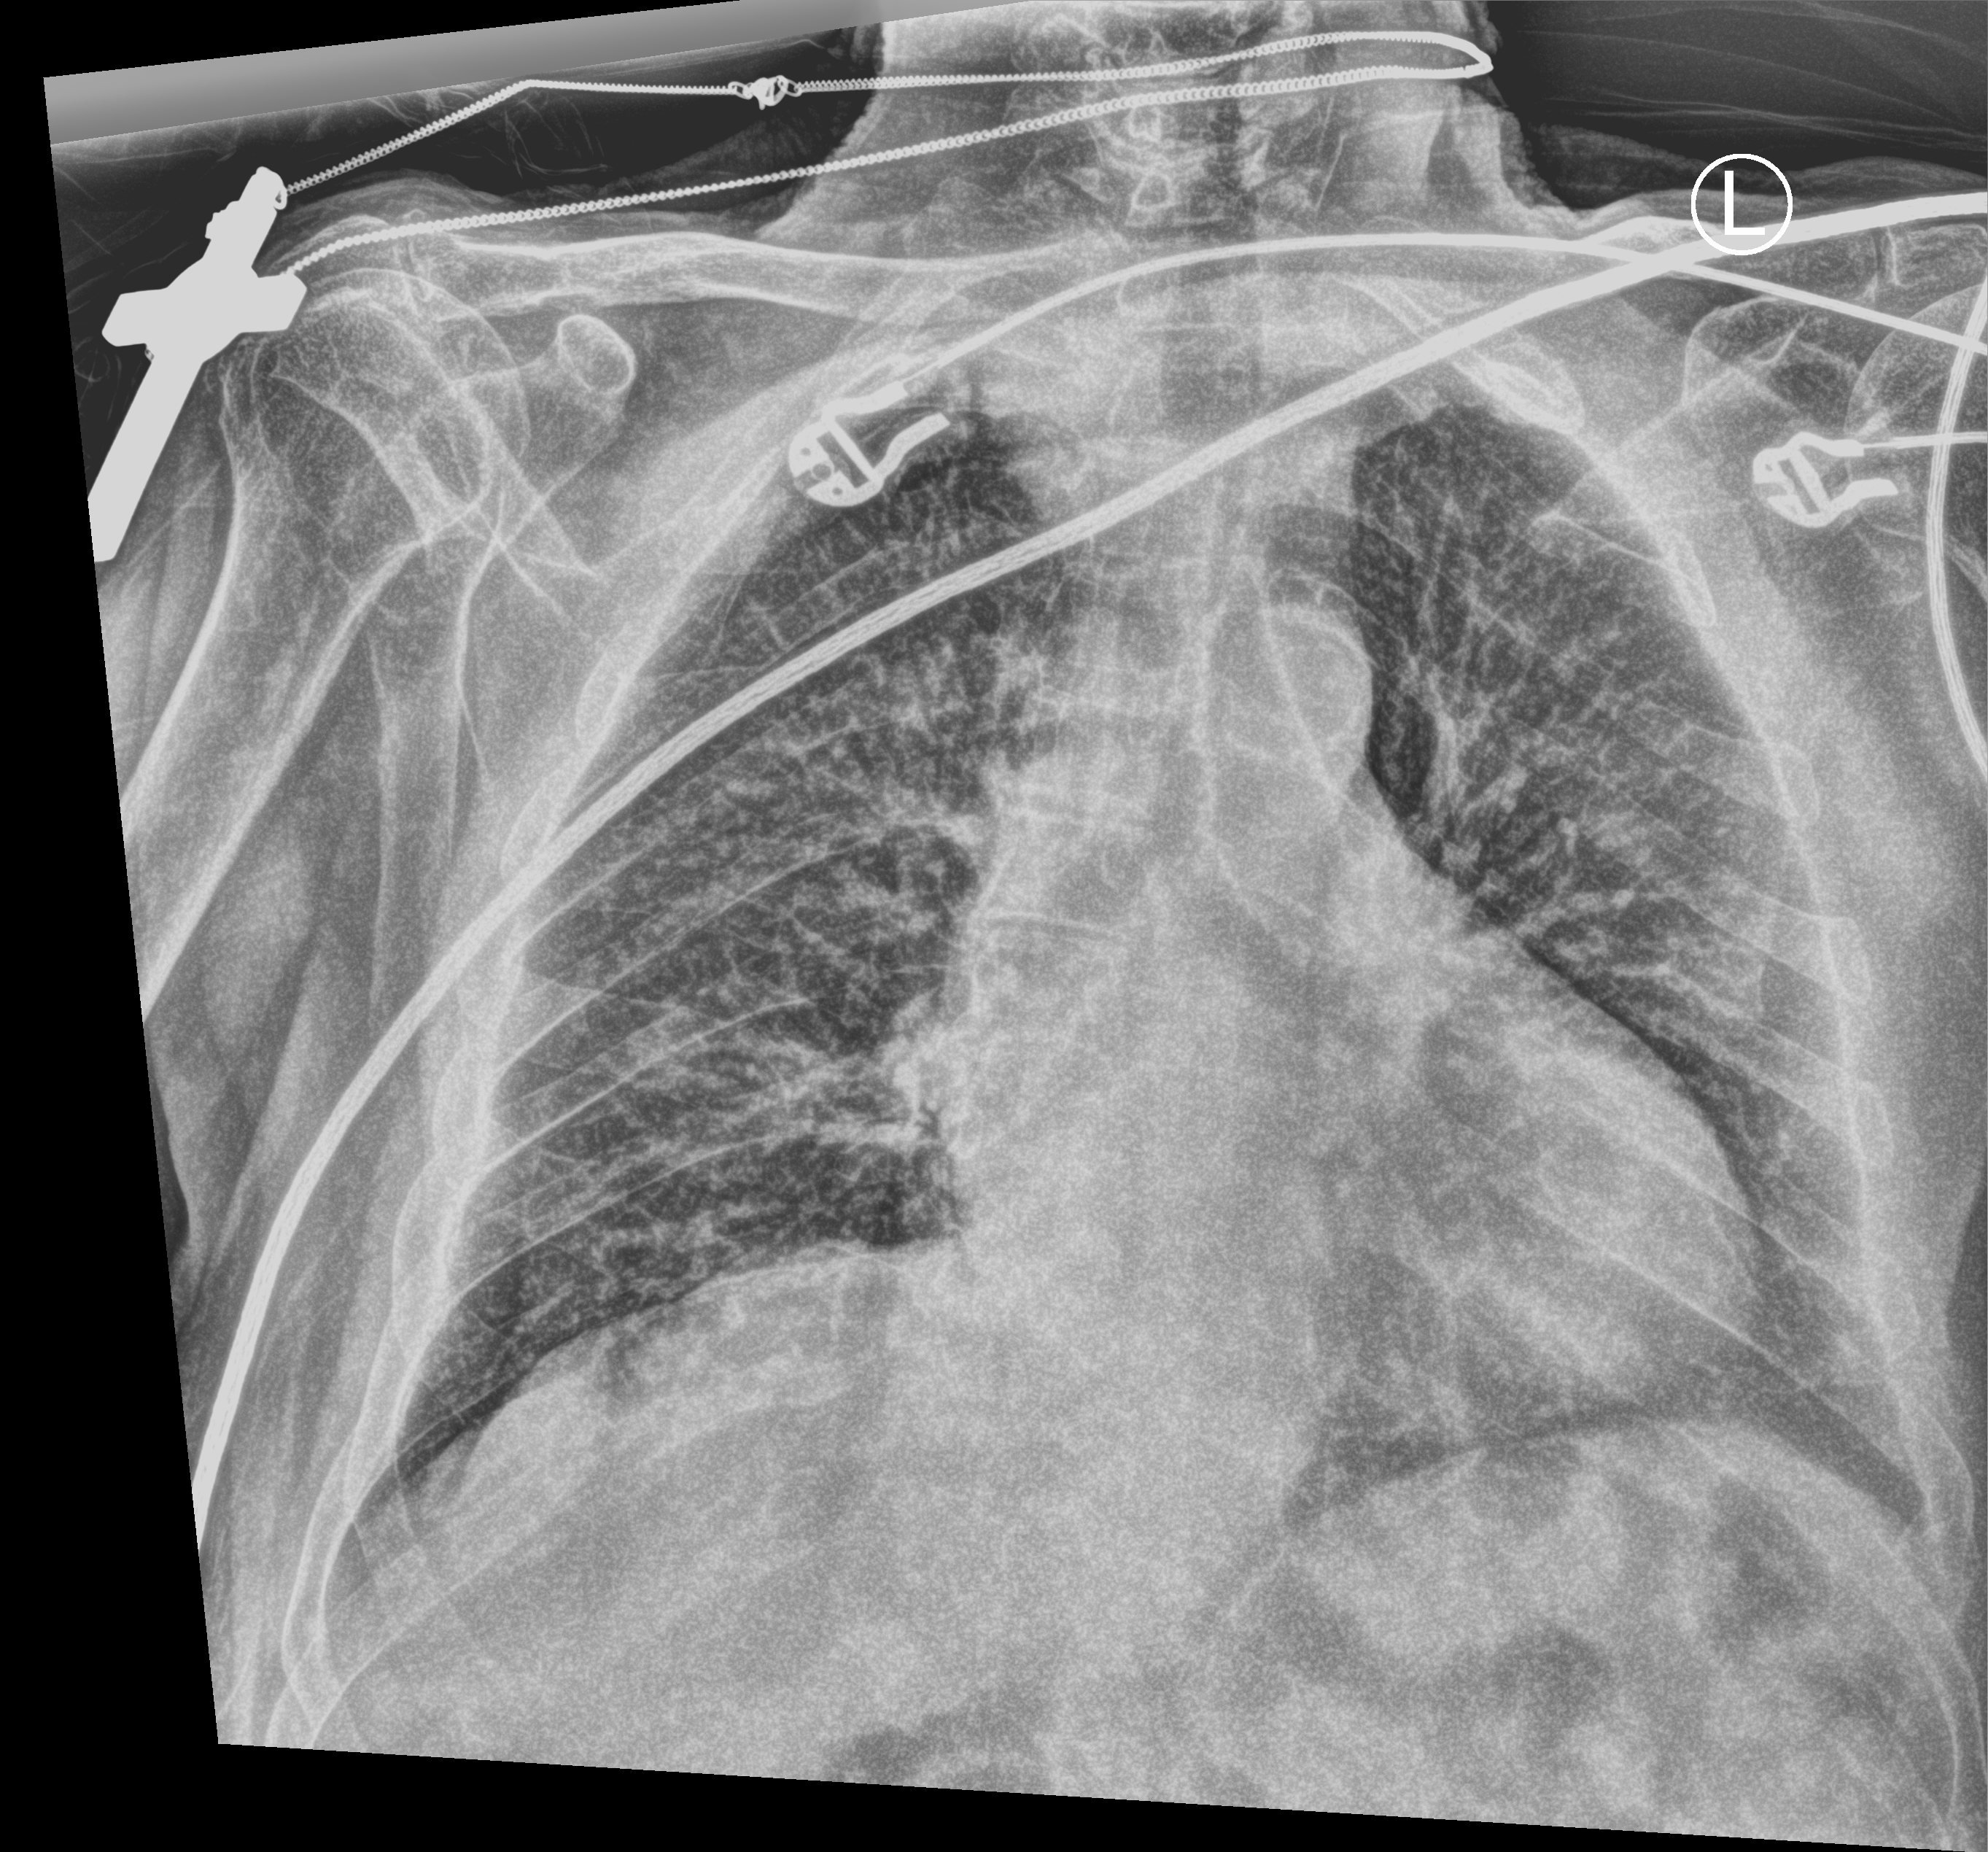
Chest X-ray (portable), anteroposterior (AP) projection. Male patient hospitalised with COVID-19, age 75–90 years.
From the hospital-stay record, not from the radiograph (when in the stay this image was taken is not recorded):
- admitted to intensive care during this hospital stay: no